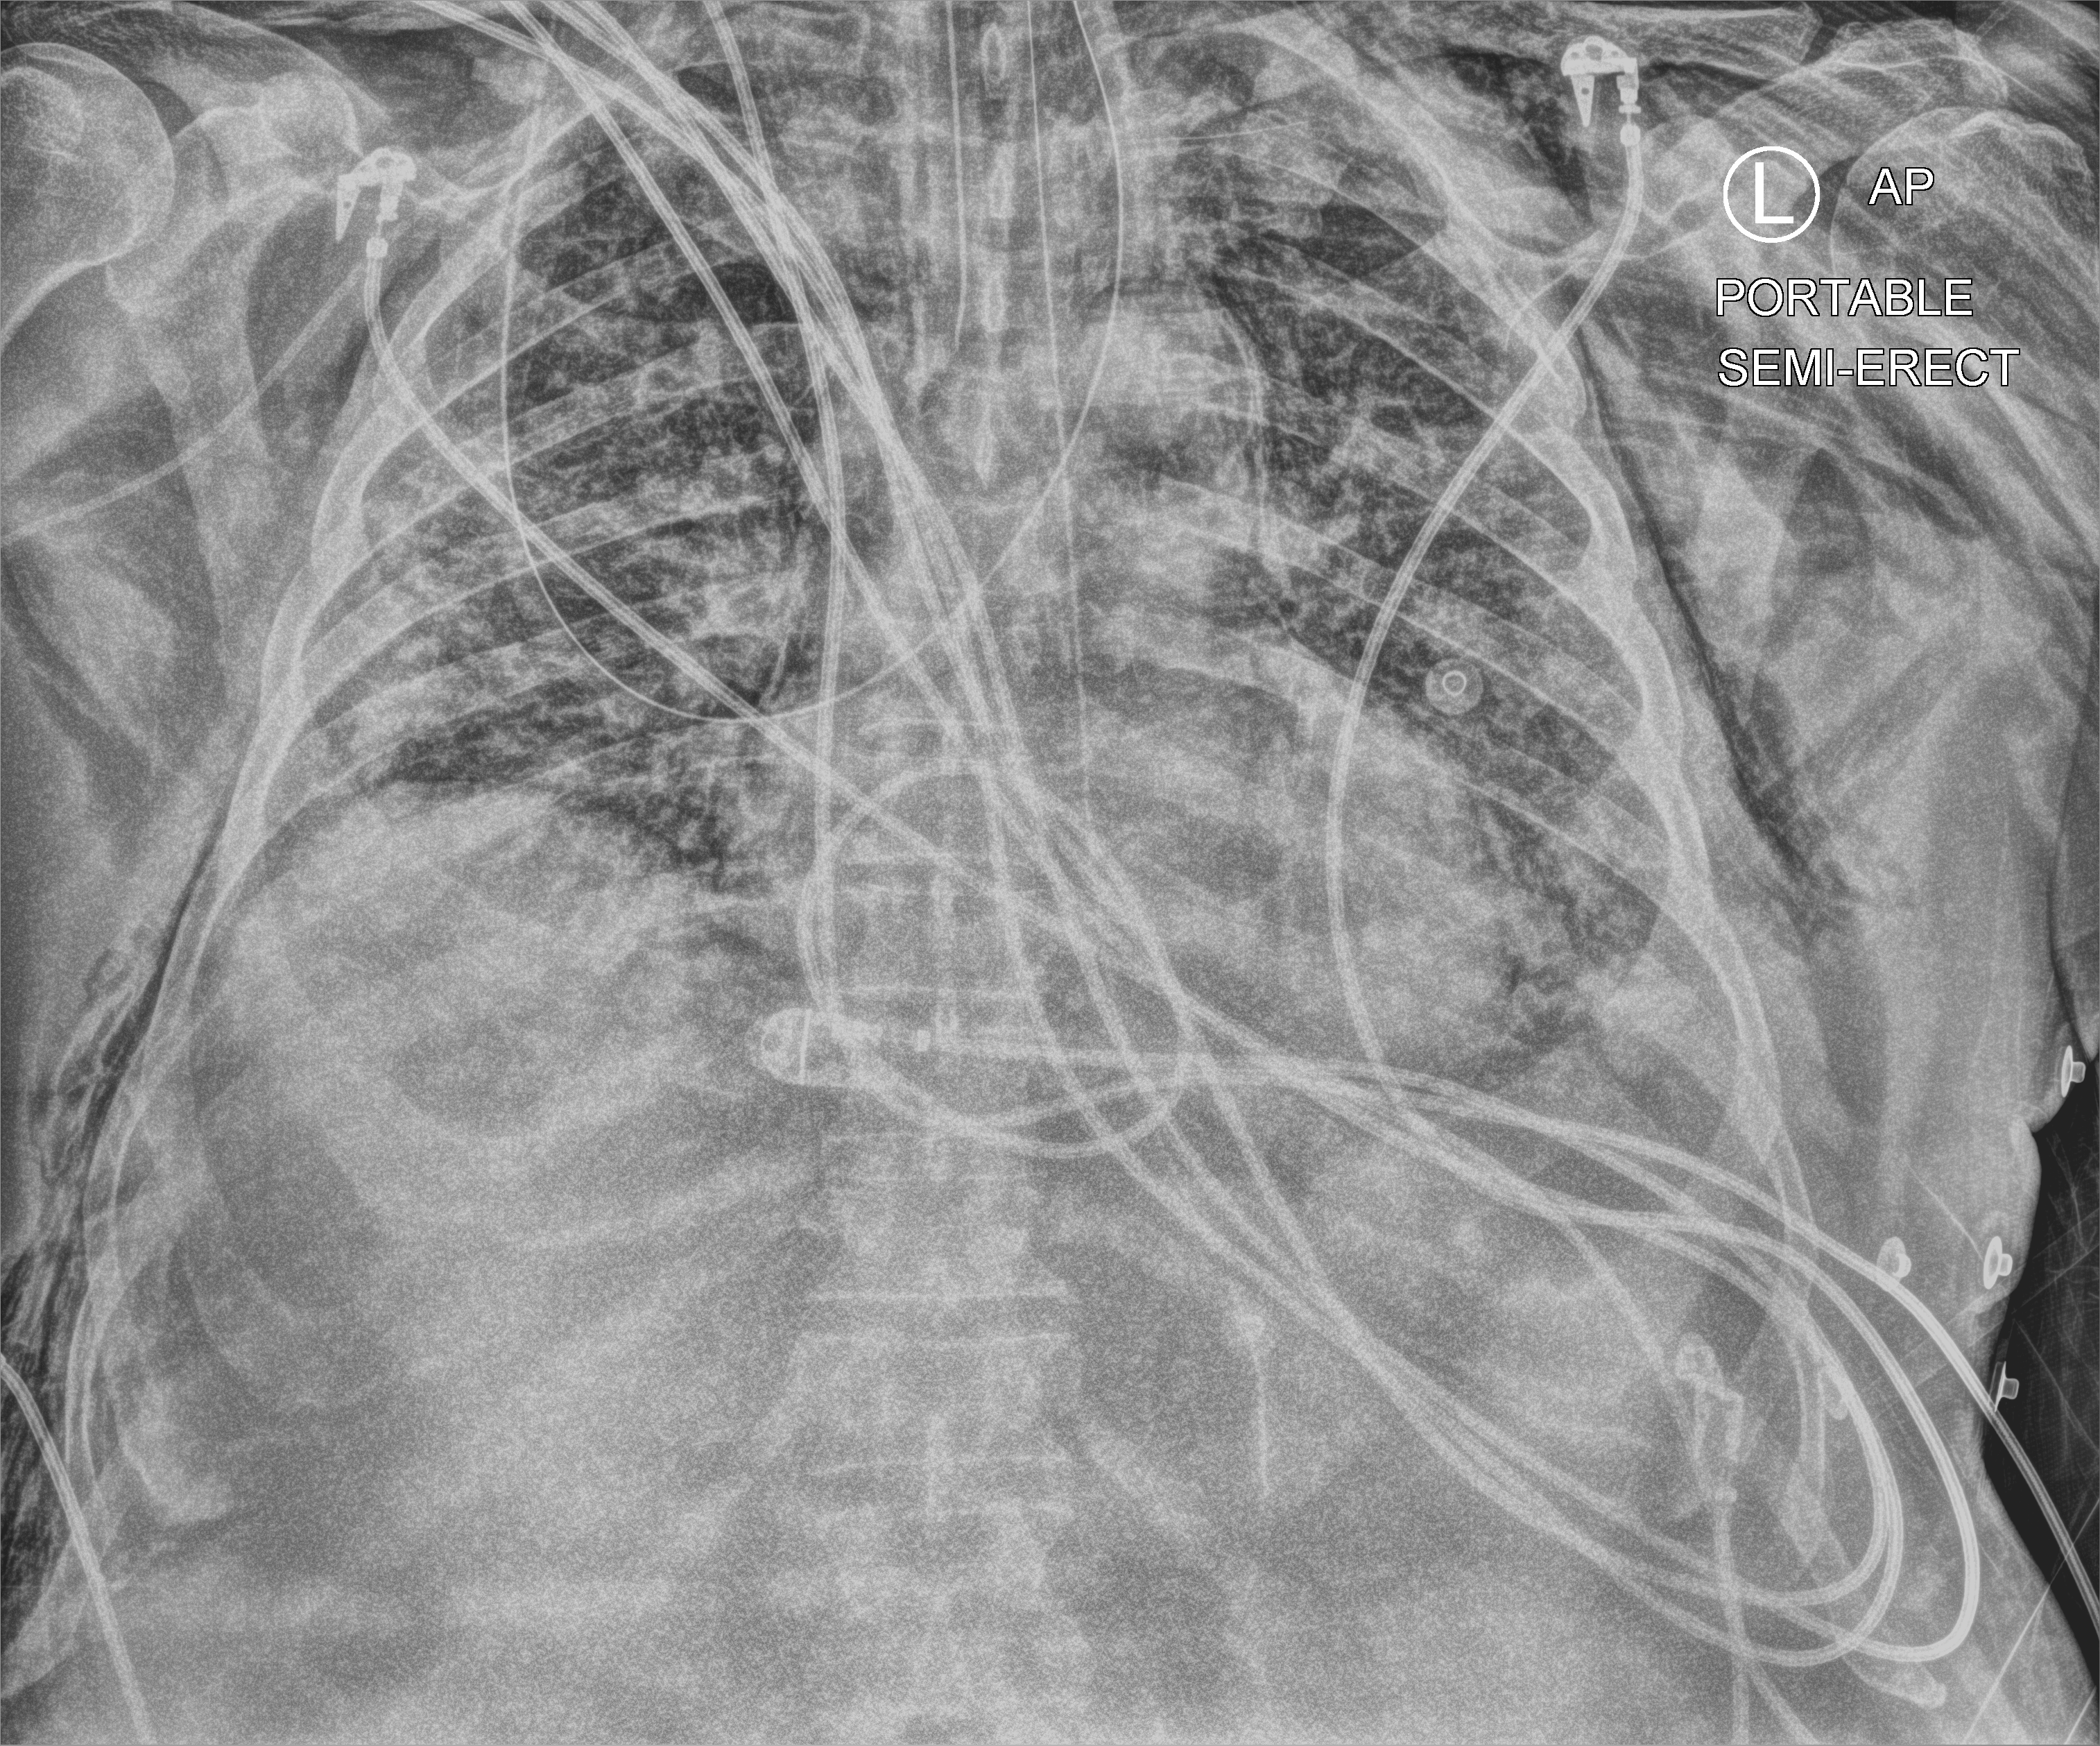
Bedside chest radiograph (computed radiography), anteroposterior (AP) projection. Patient hospitalised with COVID-19; male, aged 60–74 years.
Admission-level facts for this patient (not findings on this image; timing relative to this image not recorded):
- mechanically ventilated during this hospital stay: yes